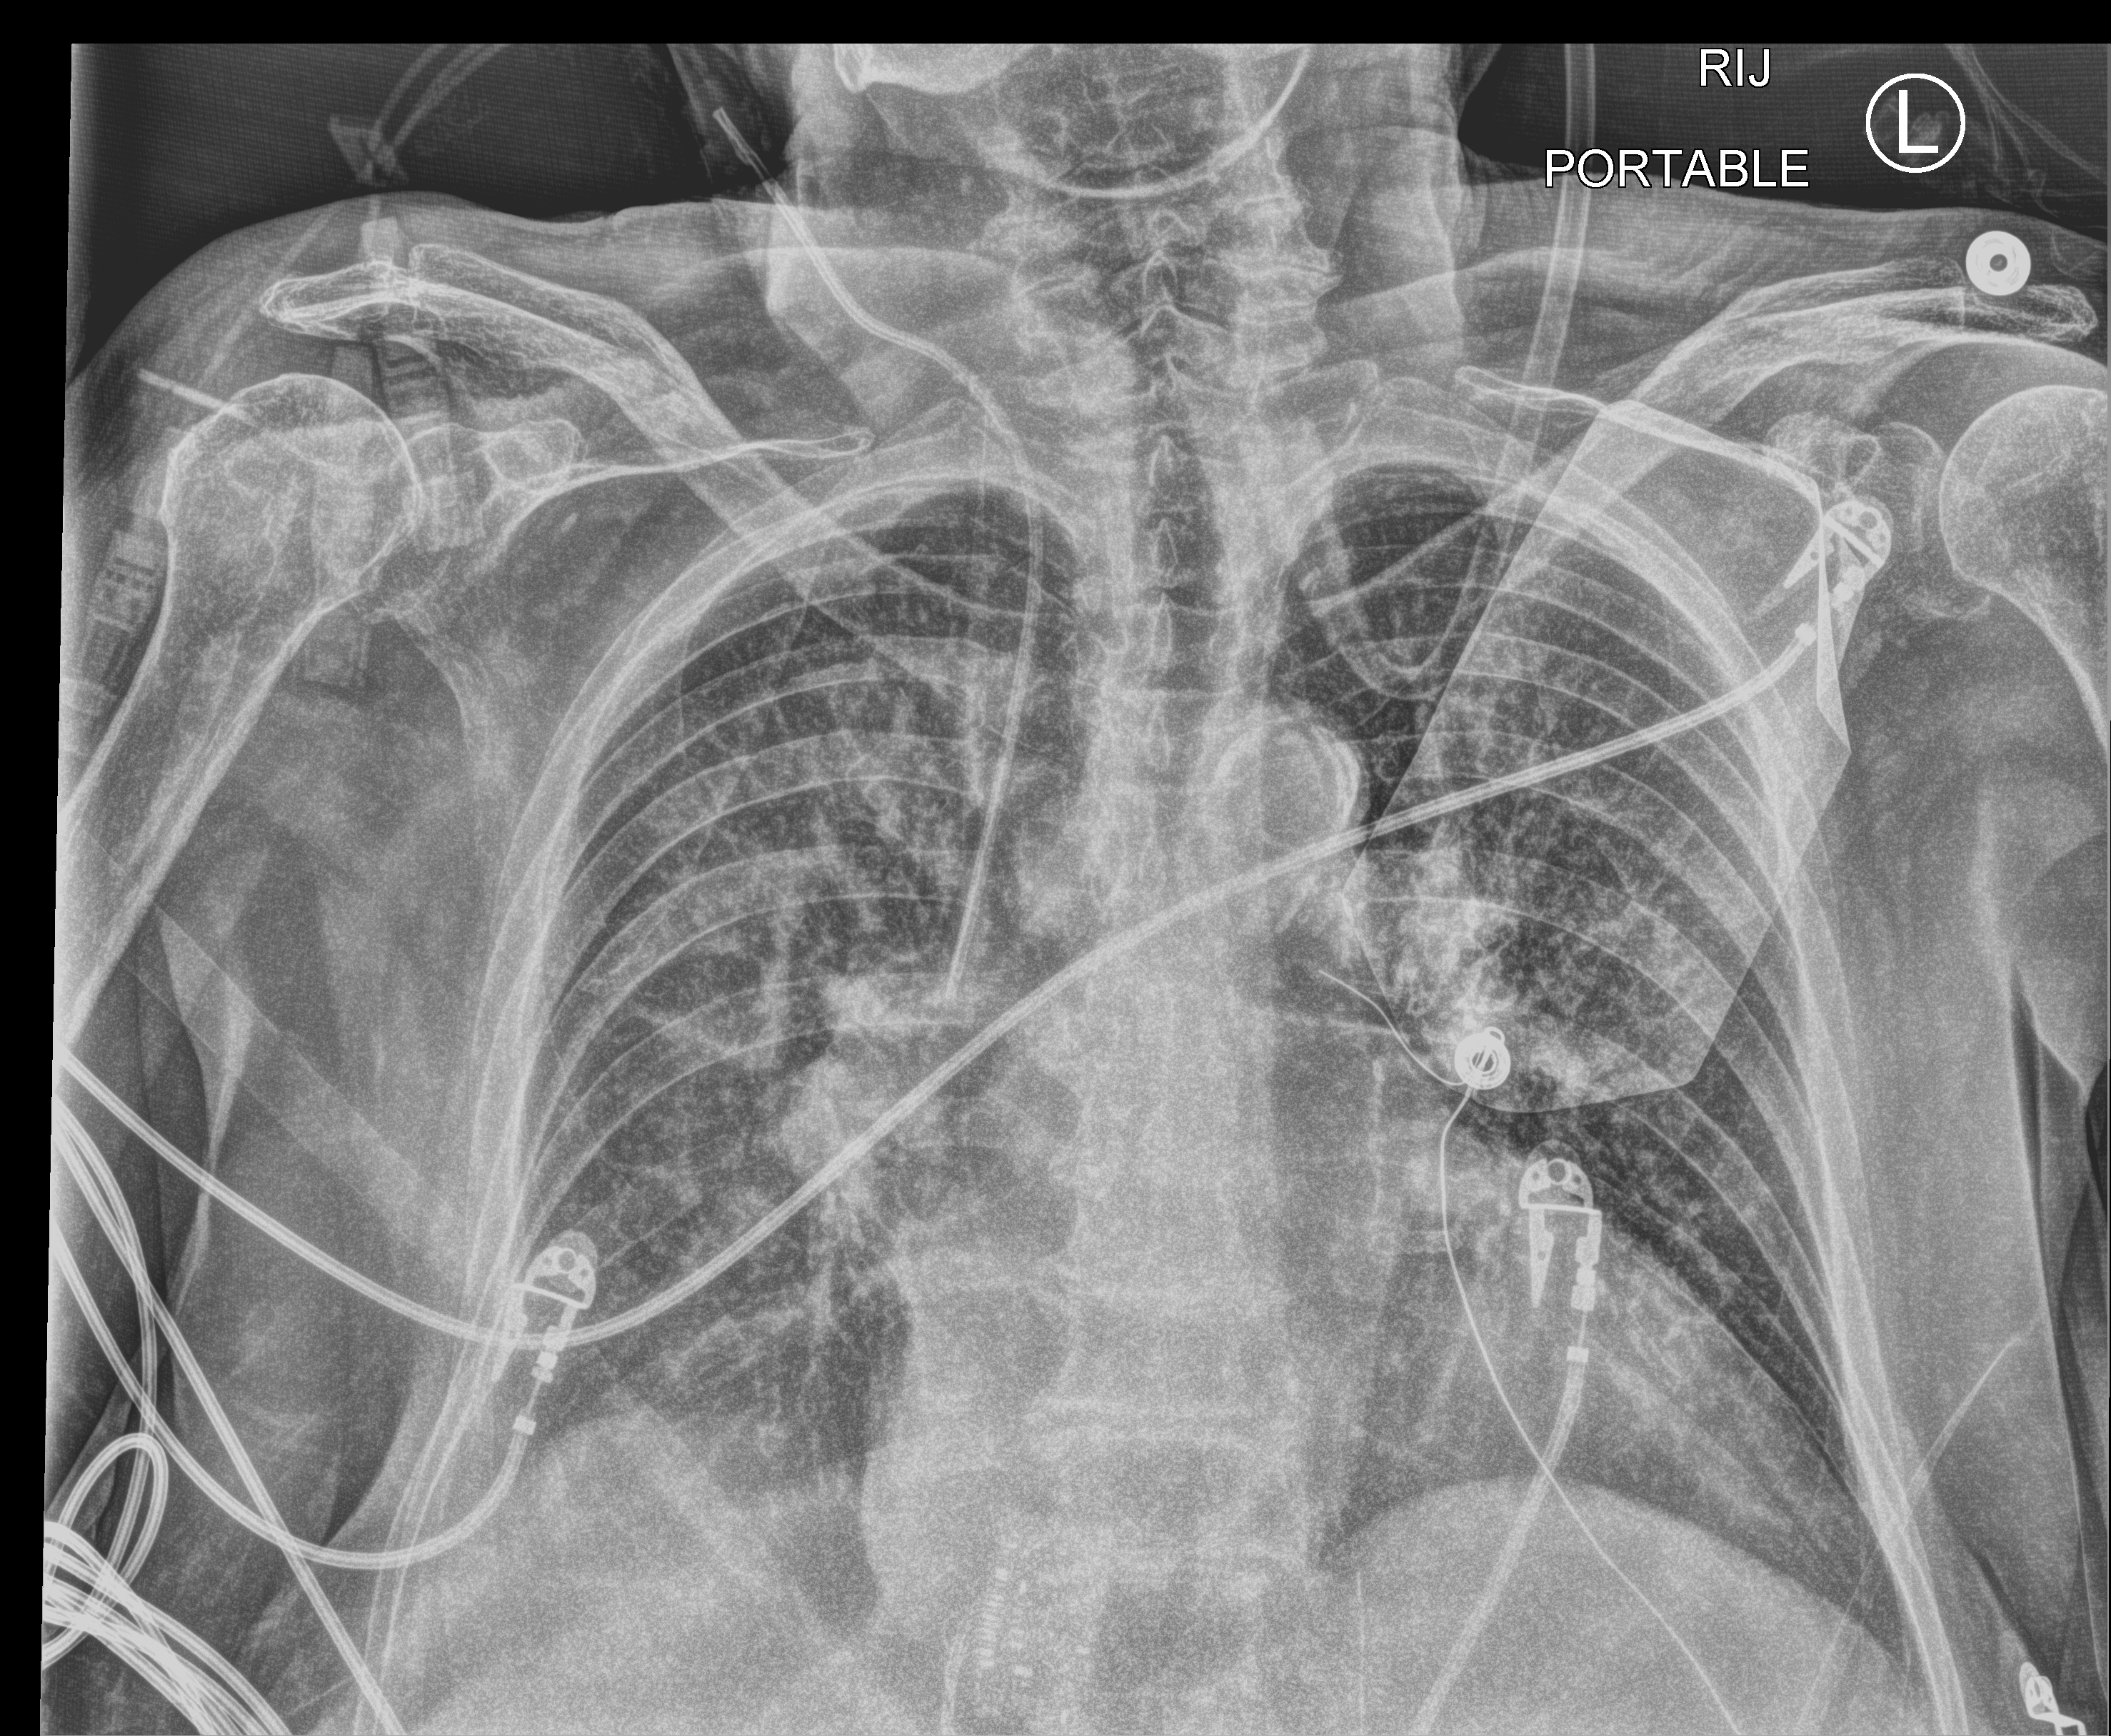
Bedside chest radiograph (computed radiography). Patient hospitalised with COVID-19; female, aged 75–90 years.
From the hospital-stay record, not from the radiograph (when in the stay this image was taken is not recorded): mechanically ventilated during this hospital stay: no.